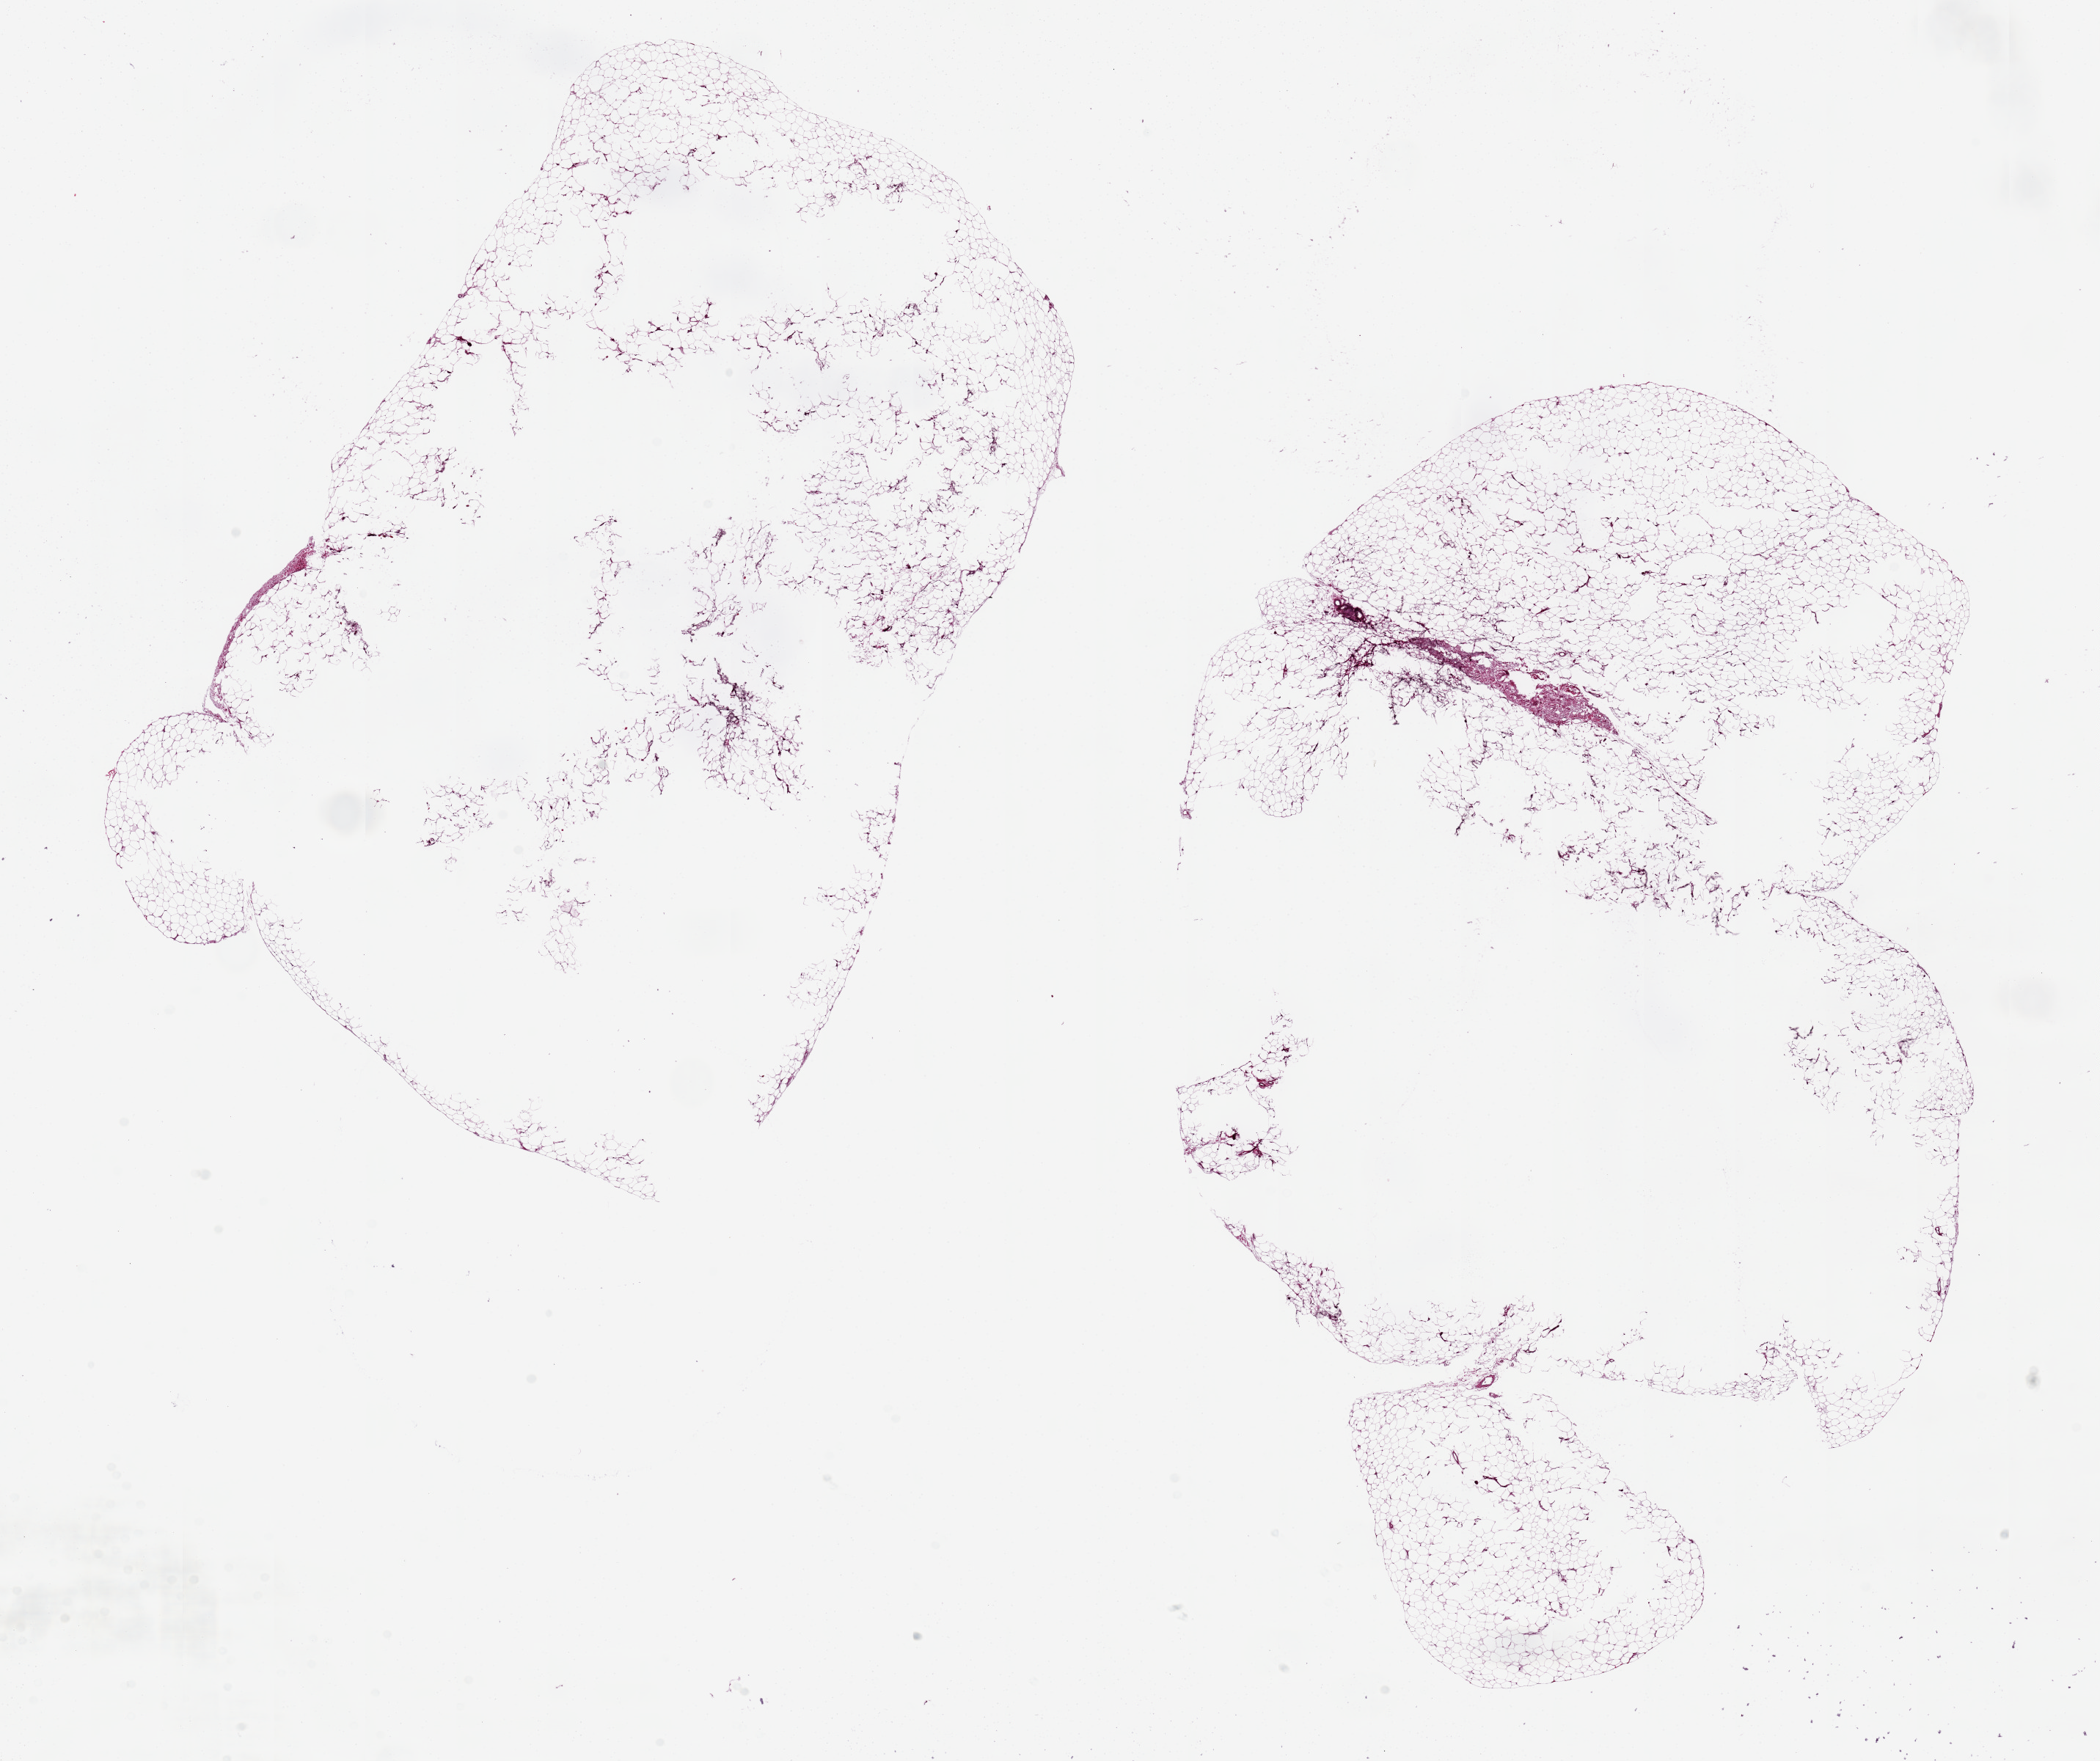
Whole-slide image, haematoxylin and eosin stain, a low-resolution overview of the entire scanned area, about 22.6 x 19.0 mm (slide scanned at 20x), PAXgene-fixed, paraffin-embedded tissue, target tissue: adipose tissue, tissue donor sample. Female donor.
• review note (as recorded): 2 pieces, ~10x10 mm; large central defects, probably fixation artifacts